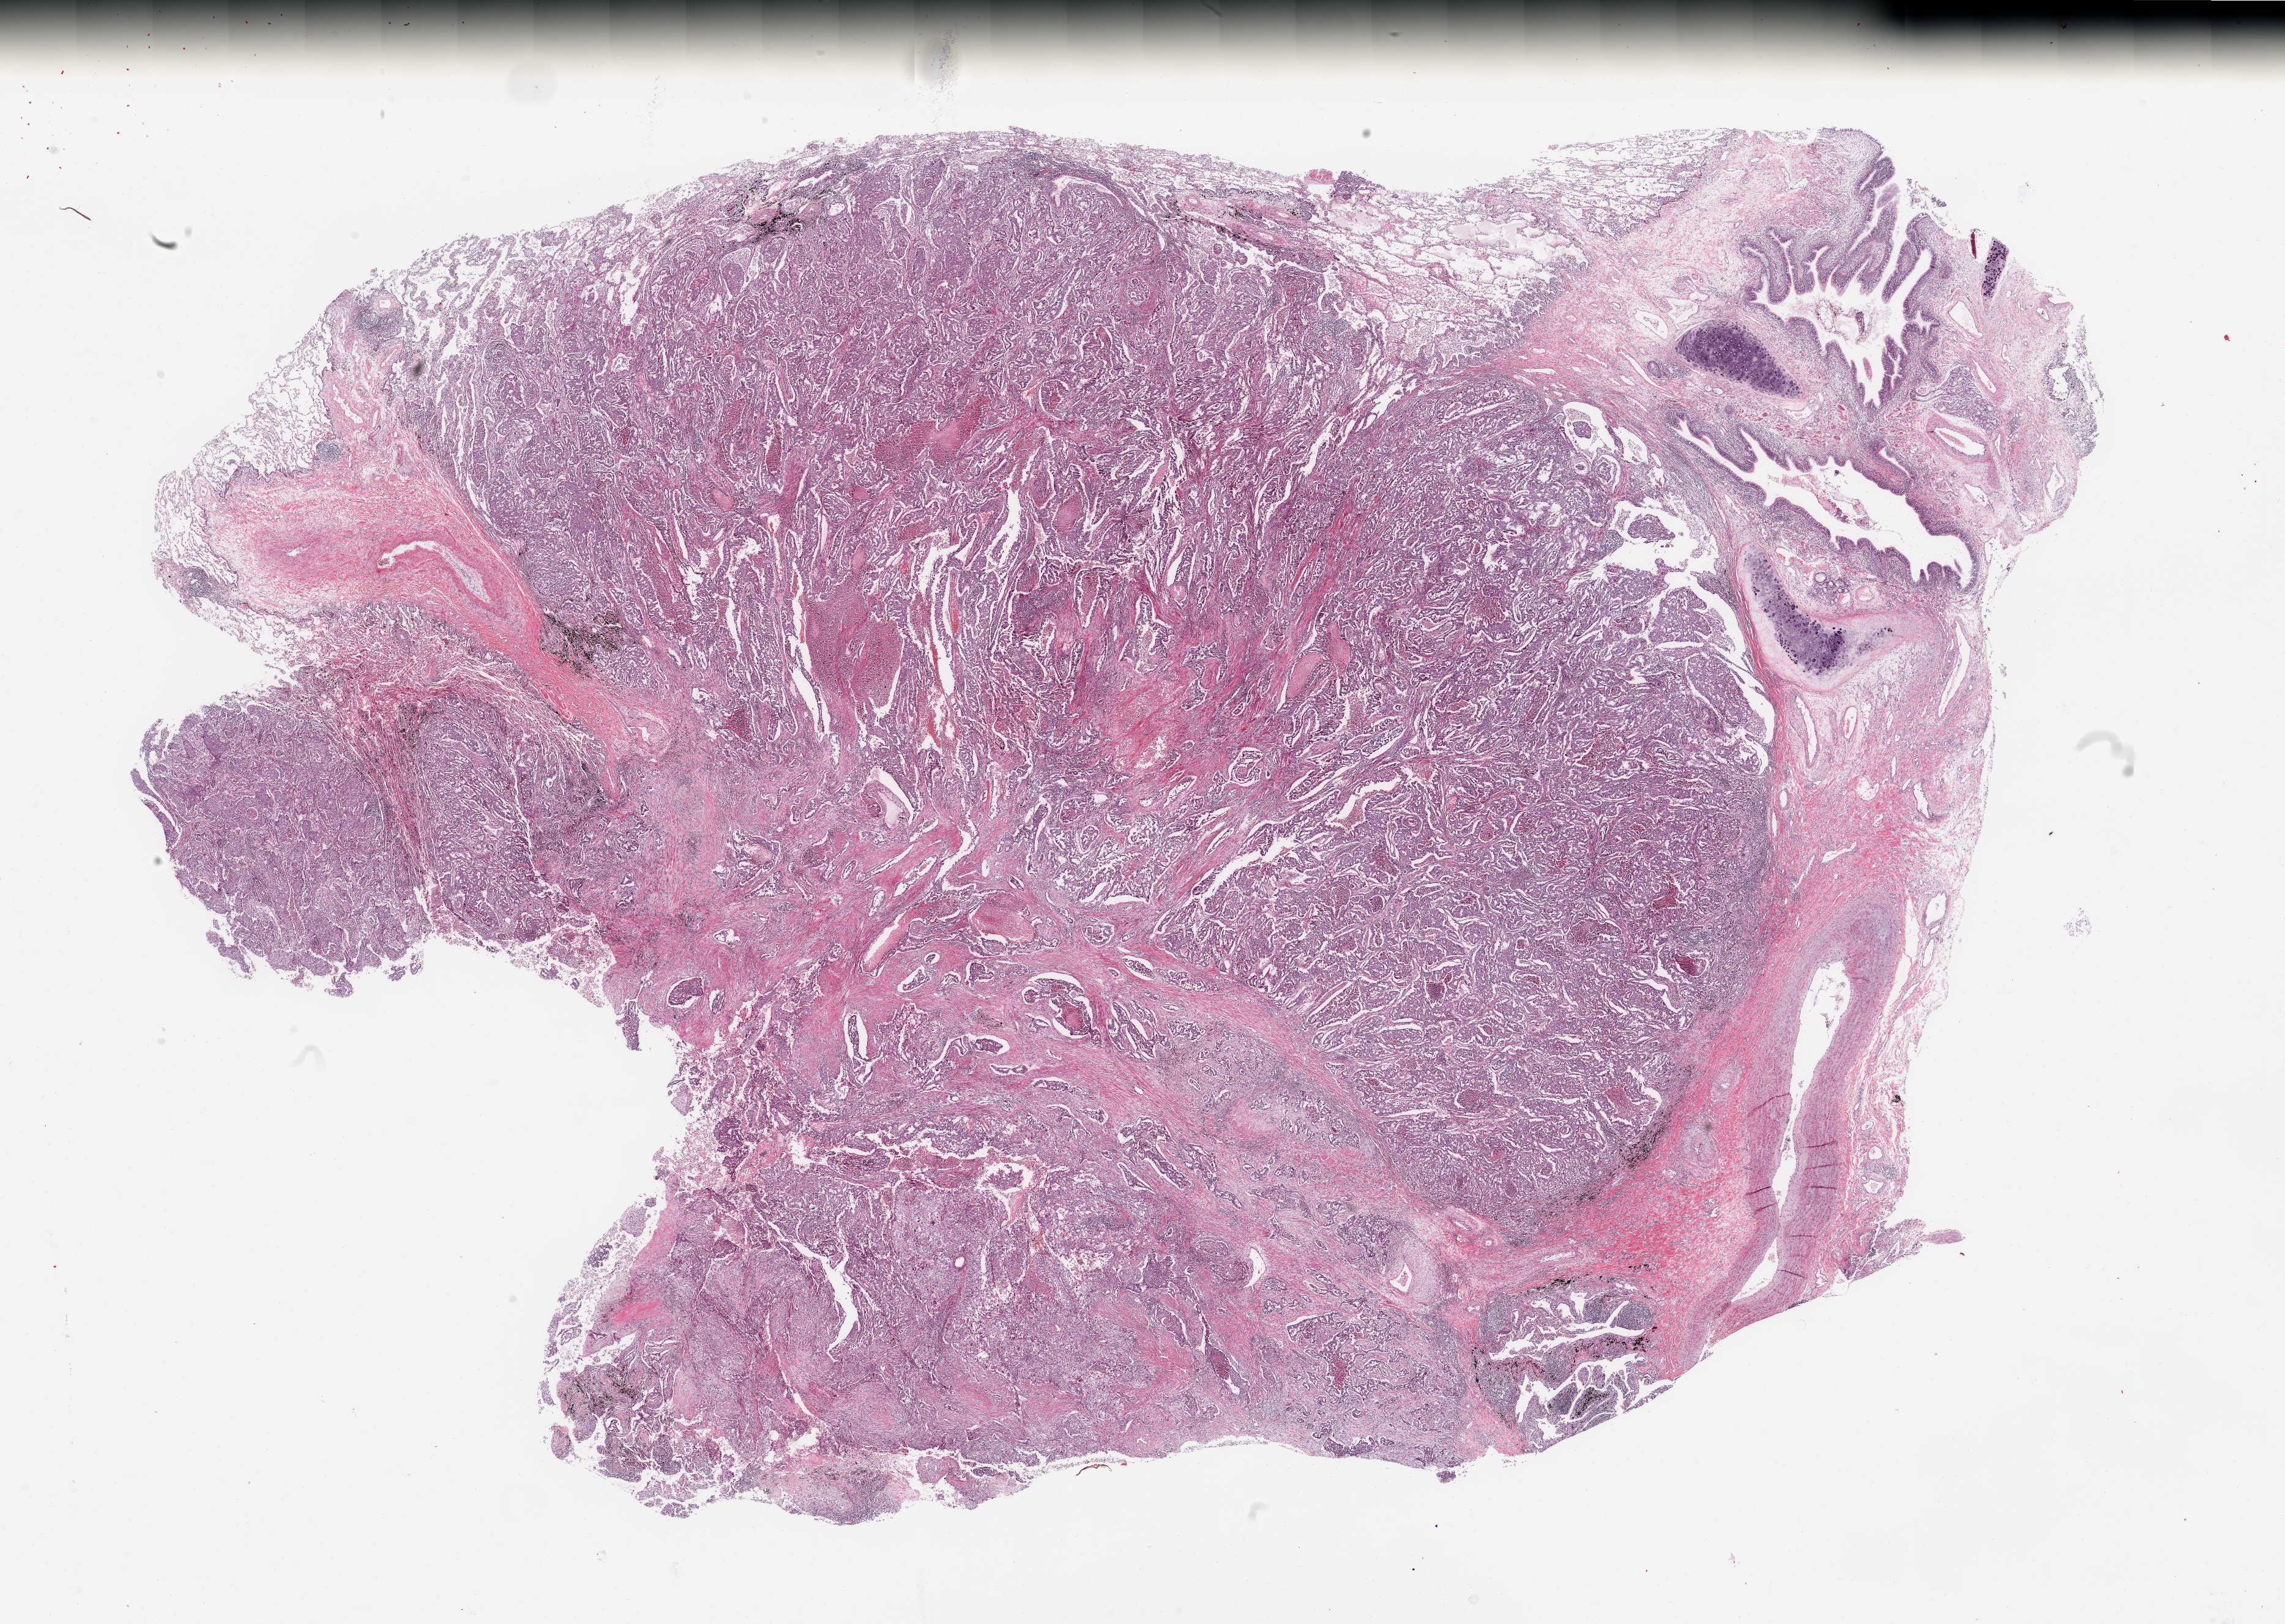
Hematoxylin and eosin (H&E) stained whole-slide image, low-resolution overview of the scanned area, about 29.5 x 21.0 mm (acquisition: 20x scan). Tumour tissue sample, lung. Male, 63 y/o. Histologic grade: G2 (moderately differentiated).
AJCC pathologic stage: IB. Diagnosis: Adenocarcinoma, NOS.